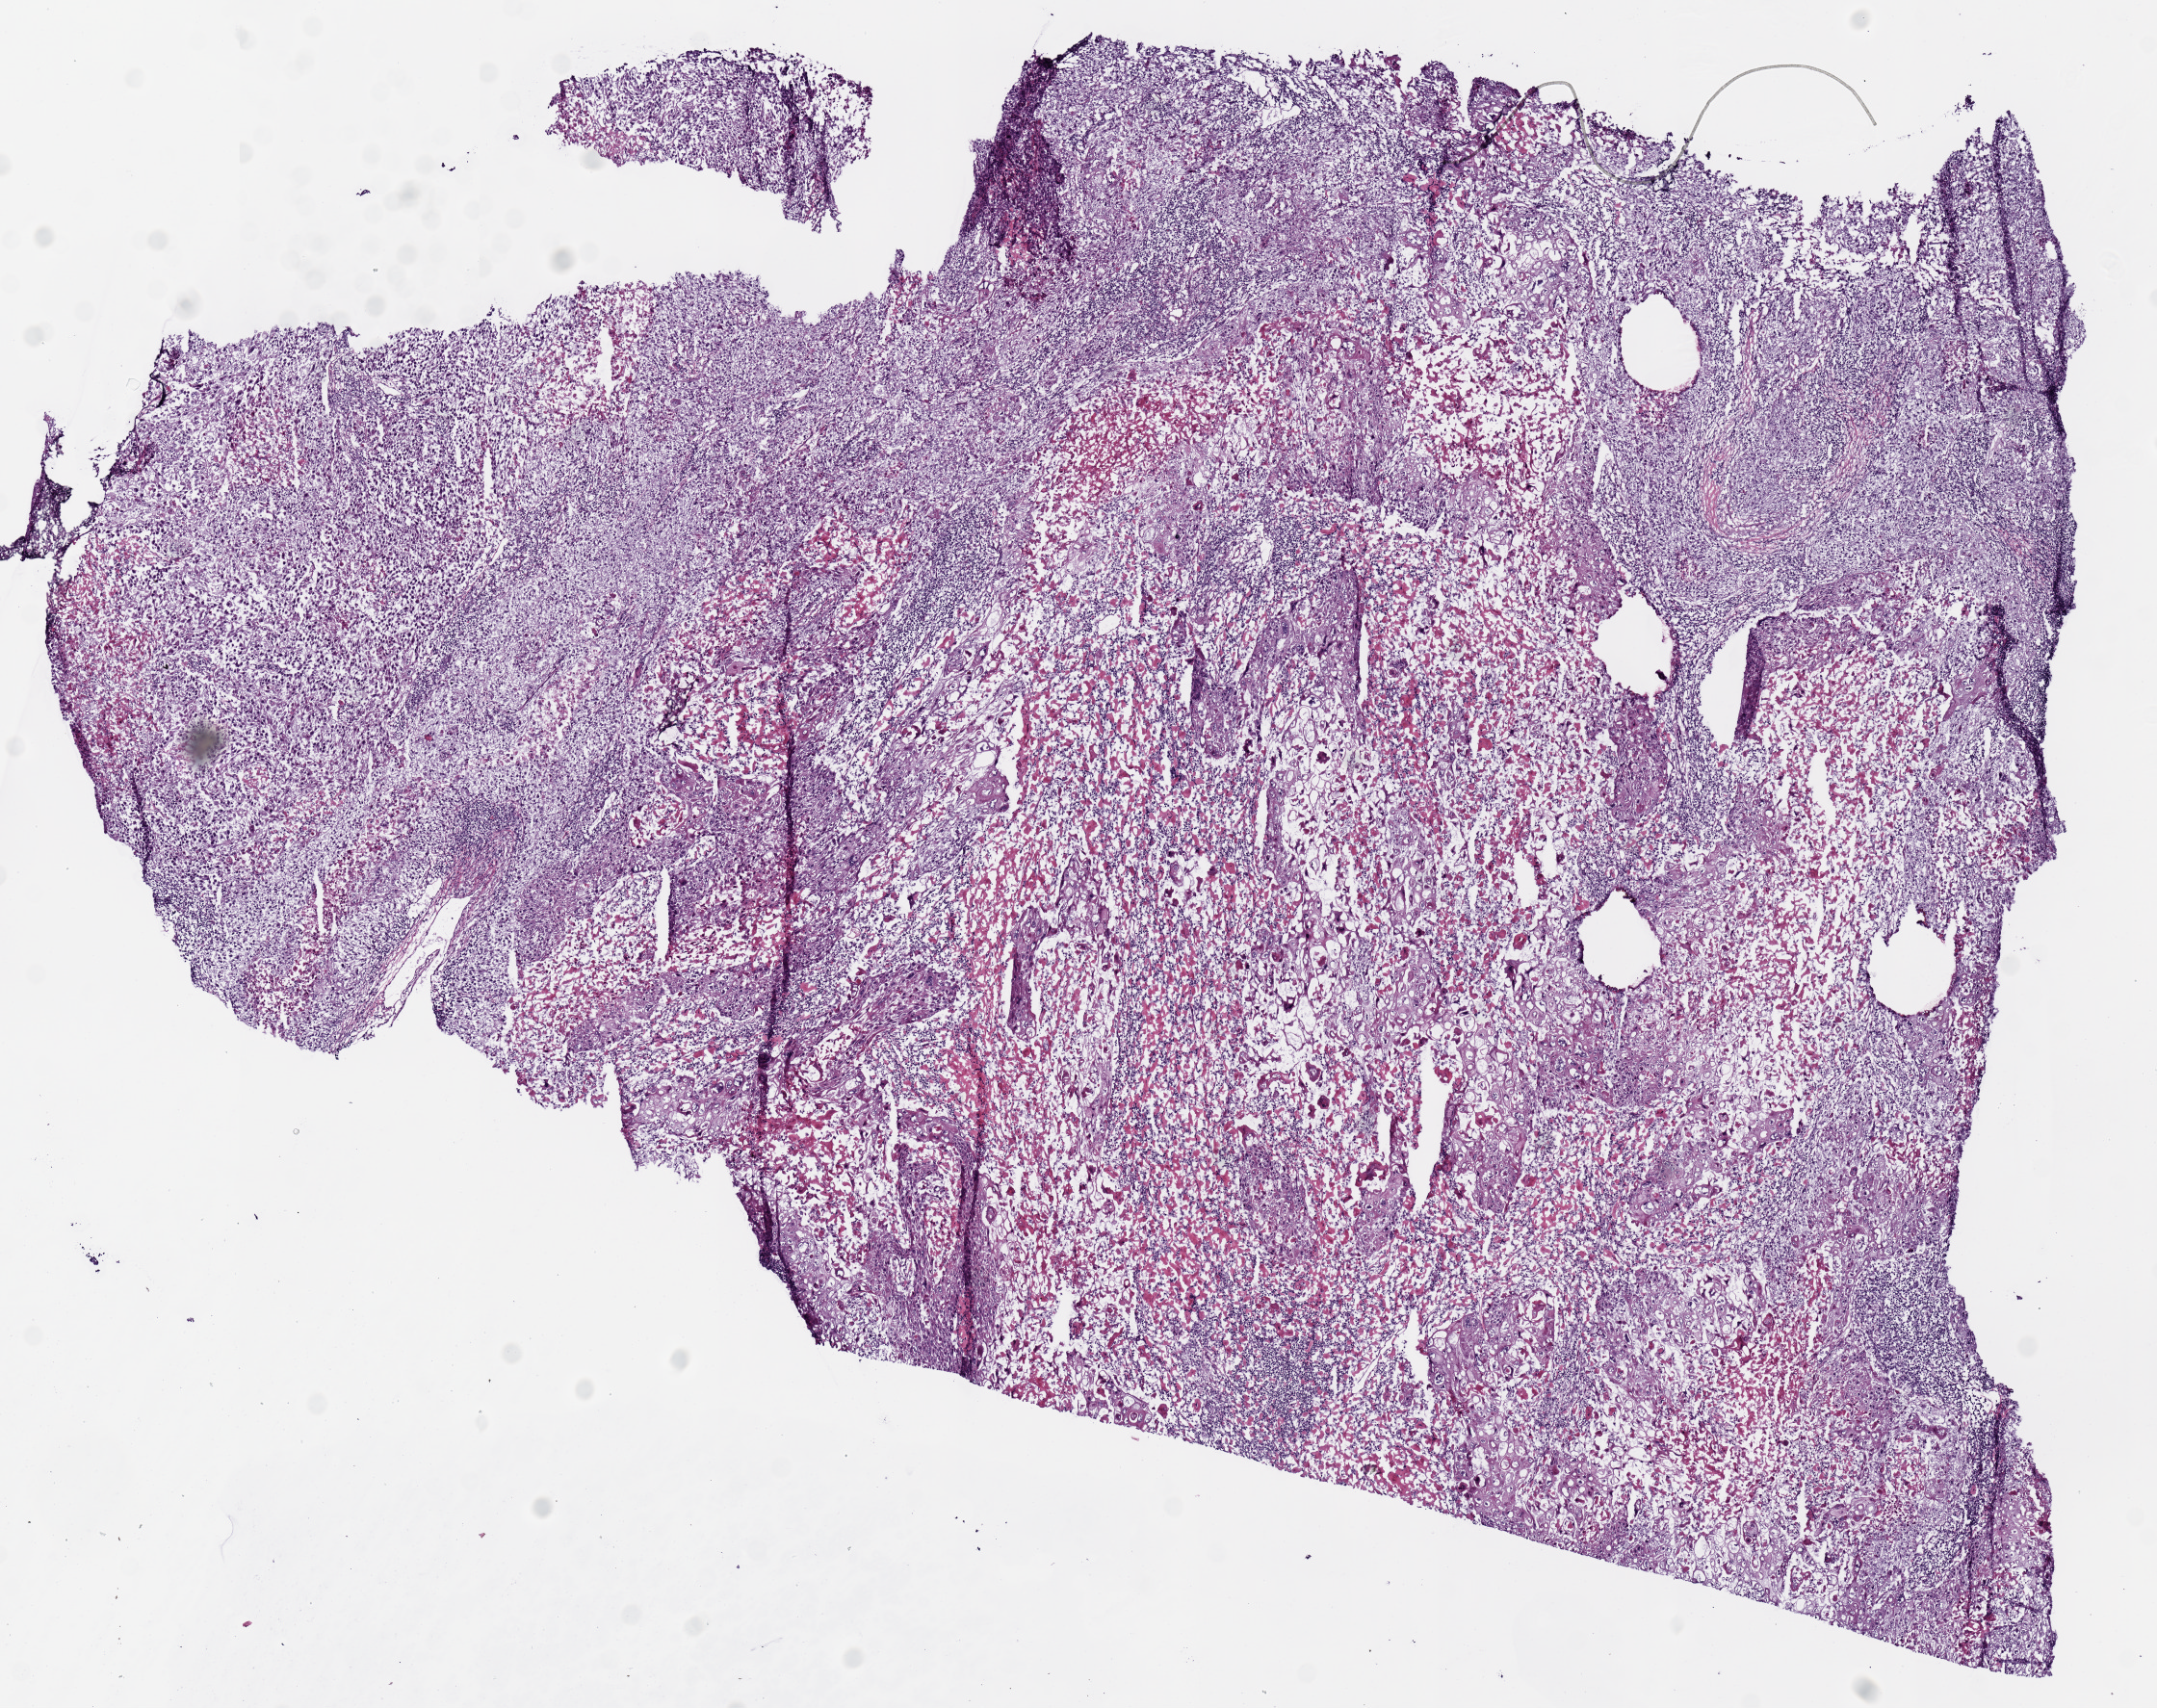
Digitized H&E tissue section (whole slide), a low-resolution overview of the entire scanned area, about 8.9 x 7.0 mm, frozen section from the top of the tissue portion, sample: primary tumour, lung. Female, age 74 years at initial diagnosis. Slide review estimates, as recorded: tumour nuclei 80%, necrosis 5%.
TNM: T3 N0 MX. Diagnosis: Squamous cell carcinoma, keratinizing, NOS (lower lobe, lung). AJCC pathologic stage: IIB (7th edition).